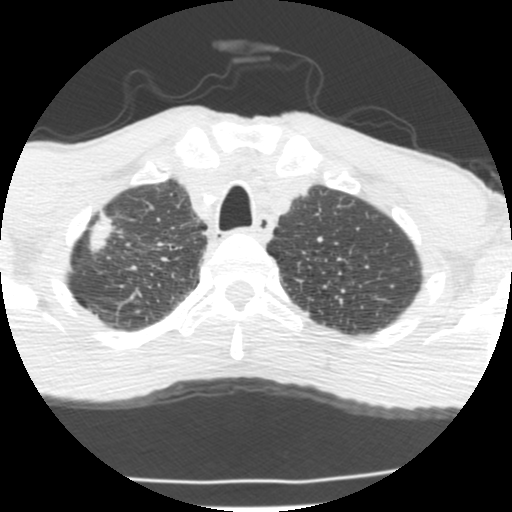
Axial slice from a low-dose chest CT screening exam, second annual screen, lung window (W 1500 / L -600 HU), 2.5 mm slice thickness, standard (soft-tissue) reconstruction kernel (STANDARD), slice 33 of 214 in the series. Male, age 62 years at enrolment. Current smoker at enrolment.
Expert-annotated lung lesion, box from (x=63, y=214) to (x=135, y=272) px. The exam's reader record, not a measurement of the box and not confirmed to be the same lesion: non-calcified nodule or mass ≥4 mm, right upper lobe, 23 × 11 mm, spiculated (stellate) margins, soft tissue attenuation, pre-existing on the prior screen: yes.